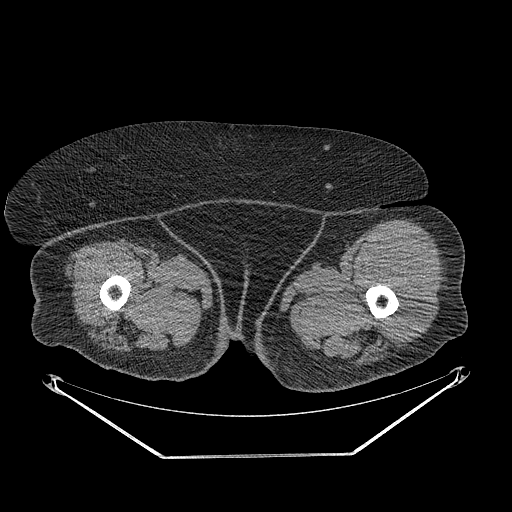
CT of an extremity soft-tissue mass (from a PET/CT study), one axial slice; reconstruction kernel STANDARD; soft-tissue window (W 400 / L 40 HU); 512 × 512 image matrix, field of view 500 × 500 mm. Female patient. Case-level facts recorded for this patient, not image findings: histological type: undifferentiated – high grade; grade: high; site of the primary tumour: left thigh.
Annotated regions visible in this slice (expert contour drawn on MRI and transferred to this co-registered scan by the dataset authors):
- gross tumour volume including surrounding oedema: box from (x=372, y=249) to (x=426, y=337) px
- gross tumour volume (mass): (x=374, y=249)–(x=426, y=336)